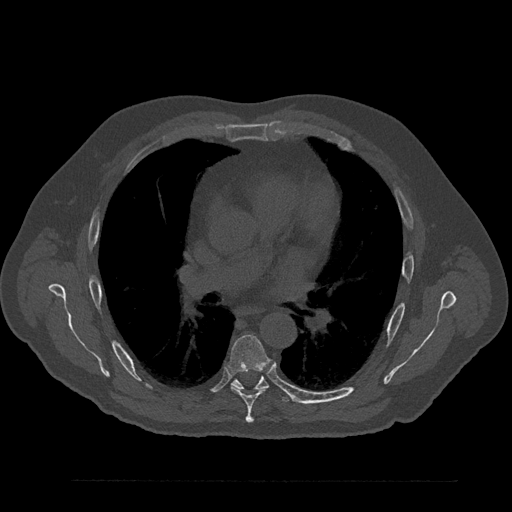
CT including the spine, one axial slice; position 537 of 797 along the scan axis; bone window (W 1800 / L 400 HU); 0.5 mm slice thickness; 512 × 512 image matrix. Patient: male, 61 years. Case-level facts recorded for this patient, not image findings: primary cancer: prostate.
Annotated regions visible in this slice (semi-automatically segmented with operator editing):
- T6 vertebra: bounding box (x1, y1, x2, y2) in pixels: (228, 334, 271, 423)
- T7 vertebra: (233, 375, 290, 403)